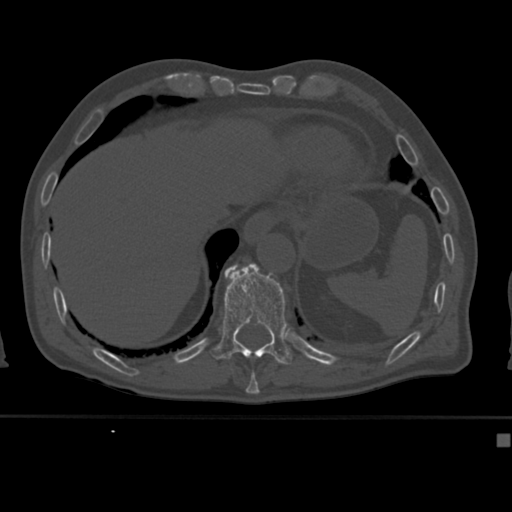
CT including the spine, one axial slice; position 213 of 430 along the scan axis; reconstruction kernel Br40s; 120 kVp; bone window (W 1800 / L 400 HU); 1.5 mm slice thickness; 512 × 512 image matrix, field of view 337 × 337 mm. Patient: male, 64 years. Case-level facts recorded for this patient, not image findings: primary cancer: uterus; vertebrae with lytic lesions (as recorded): T1, T4, T5, T7, L5.
Annotated regions visible in this slice (semi-automatically segmented with operator editing):
- T10 vertebra: bounding box (x1, y1, x2, y2) in pixels: (250, 371, 257, 382)
- T11 vertebra: (208, 263, 292, 365)
- T12 vertebra: (229, 266, 237, 271)